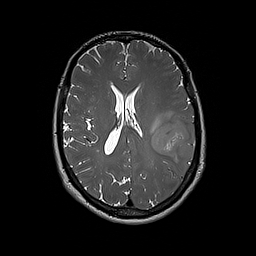
Brain MRI from a brain-tumour surgery series, one axial slice. Position 88 of 192 along the scan axis. 1 mm slice thickness. 256 × 256 image matrix, field of view 250 × 250 mm. From the clinical record (not read from this slice): histopathology: Glioblastoma; WHO grade: 4; IDH mutation: no.
Outlined on this slice (expert manual segmentation):
- tumour: bounding box (x1, y1, x2, y2) in pixels: (151, 116, 195, 165)